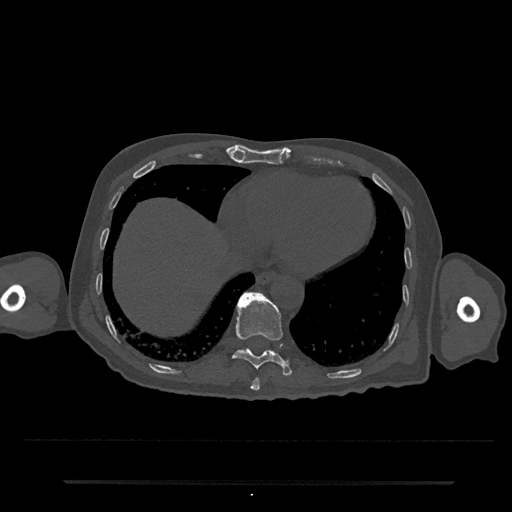
CT including the spine, one axial slice. Position 309 of 797 along the scan axis. 120 kVp. Bone window (W 1800 / L 400 HU). 512 × 512 image matrix, field of view 427 × 427 mm. Patient: male, 74 years. From the clinical record (not read from this slice): primary cancer: prostate.
Annotated regions visible in this slice (semi-automatically segmented with operator editing):
- T10 vertebra: box from (x=232, y=292) to (x=292, y=376) px
- T9 vertebra: (x=250, y=378)–(x=260, y=391)